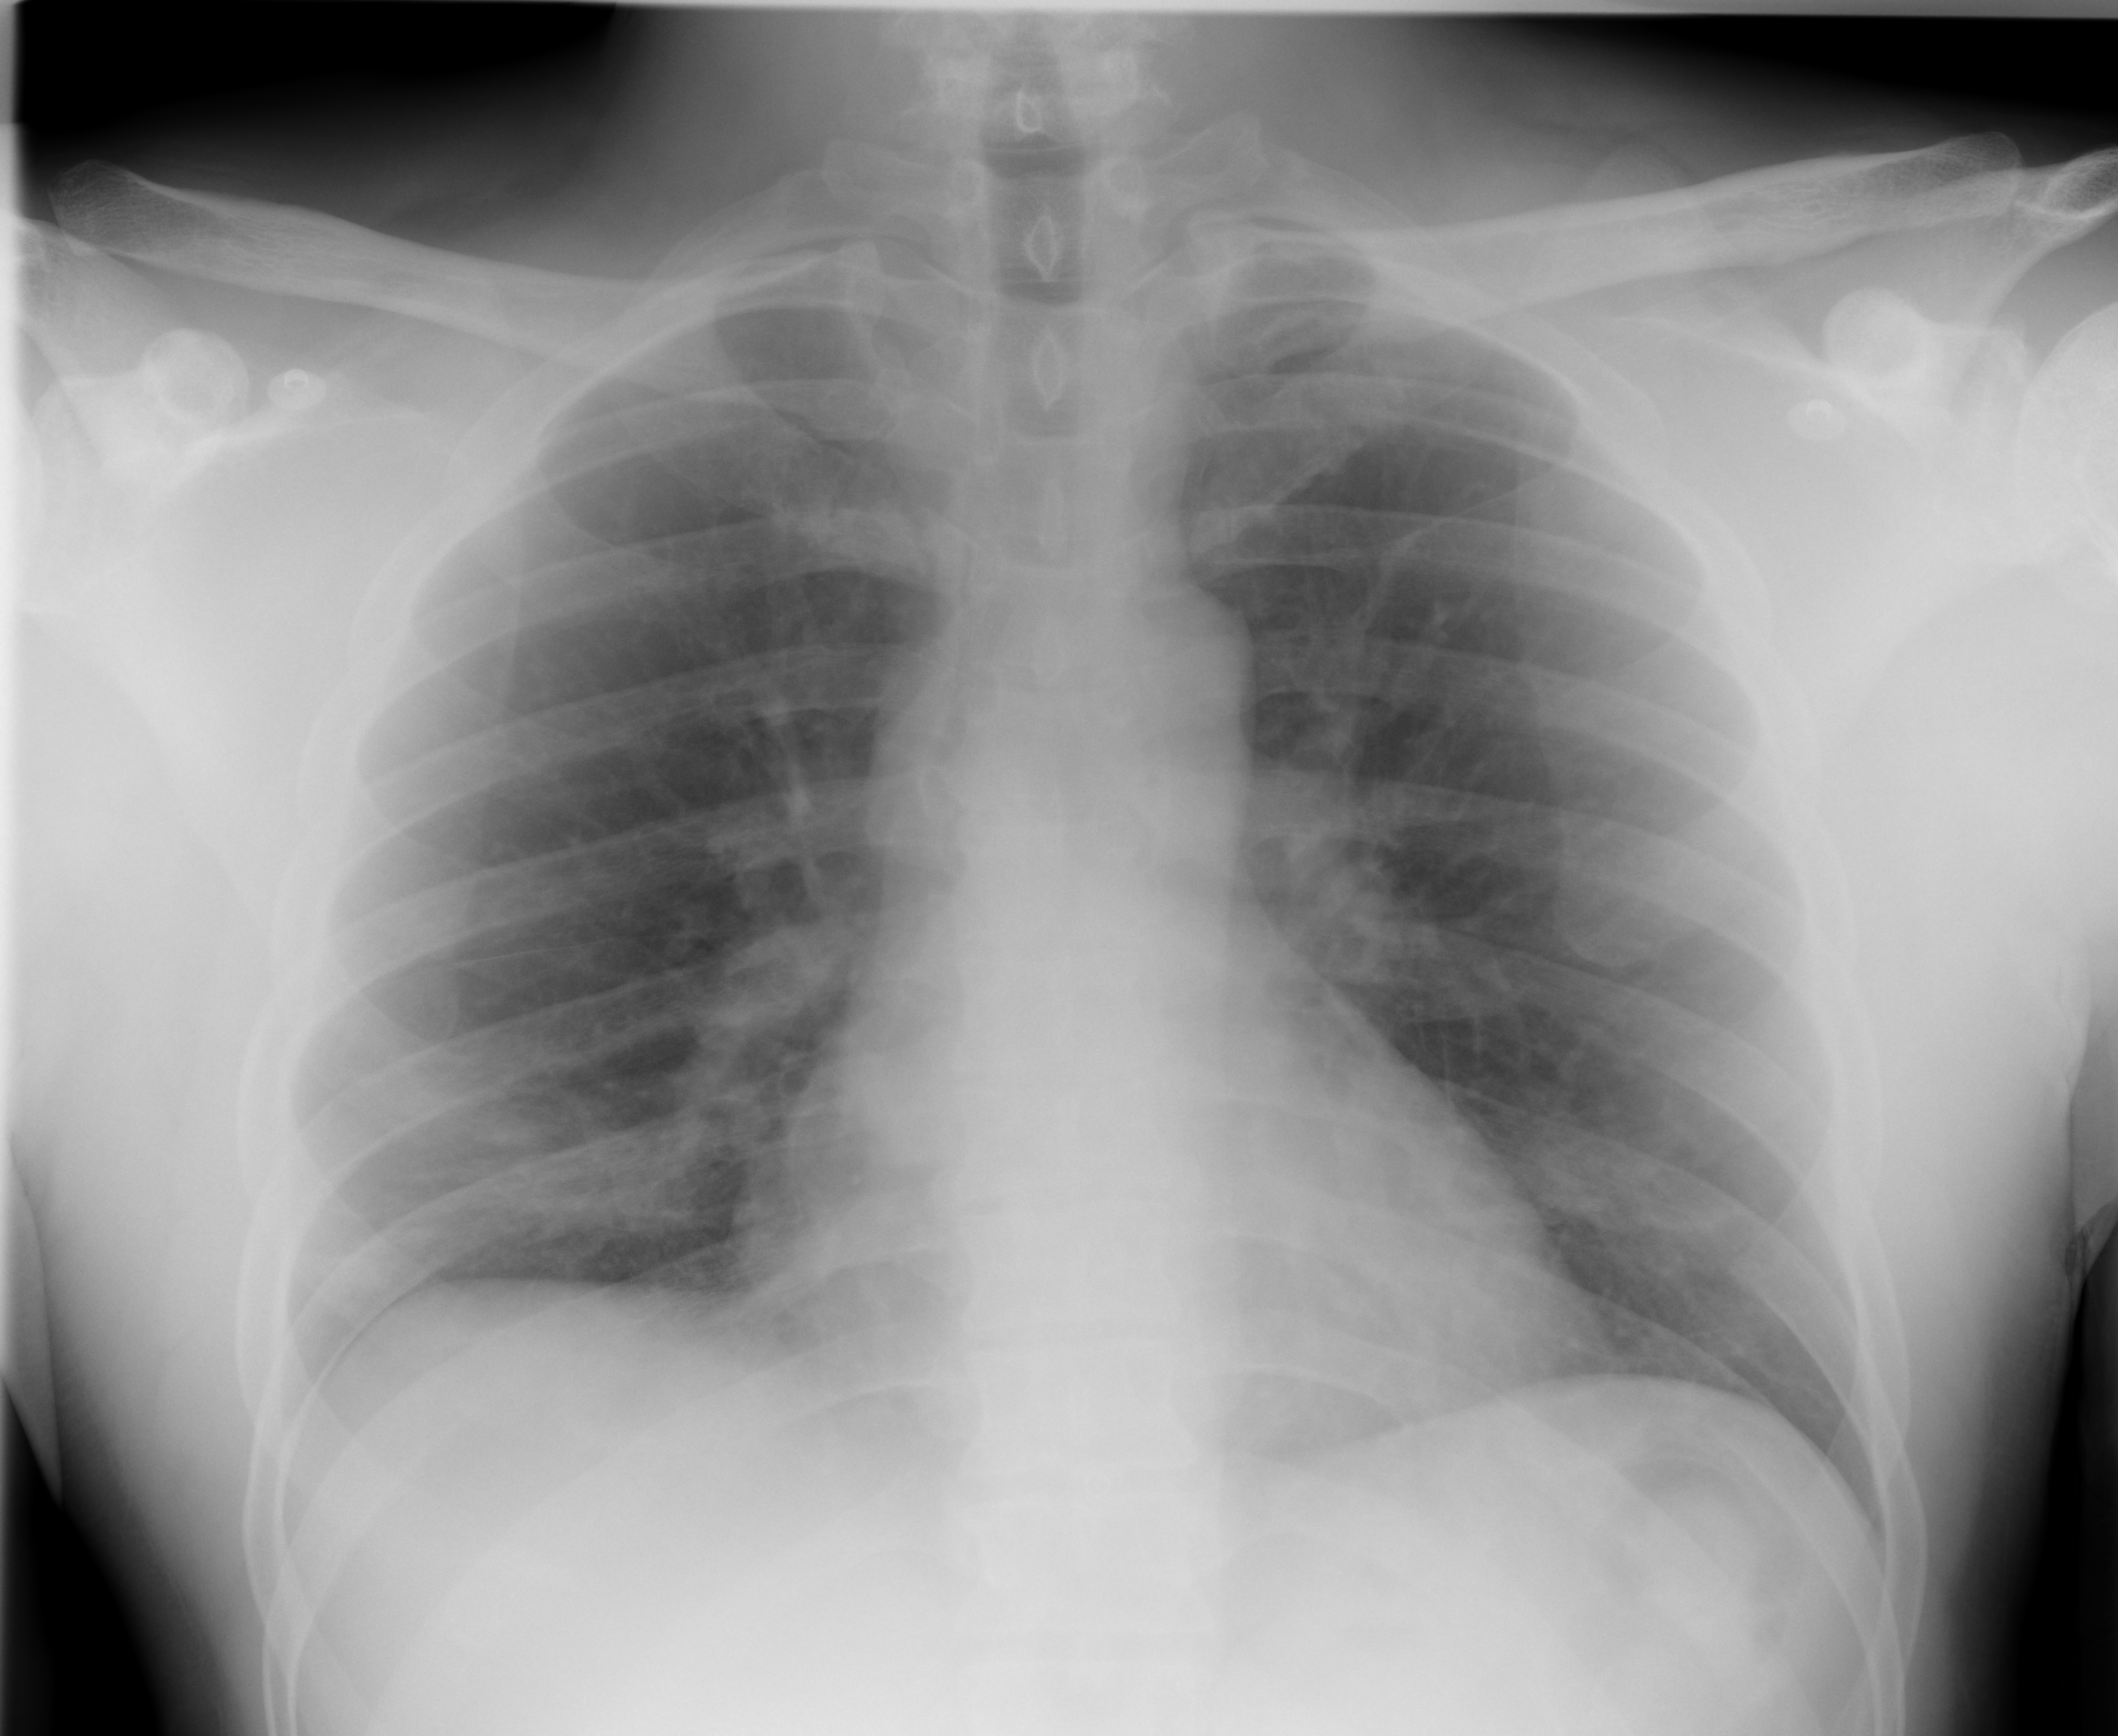
Chest X-ray (portable), AP projection. Male patient, age 44 years; imaged 6 days after the COVID-19 diagnosis.
Key findings recorded by the radiologist: hazy opacities within the right lung base and to a lesser extent within the left lung base.